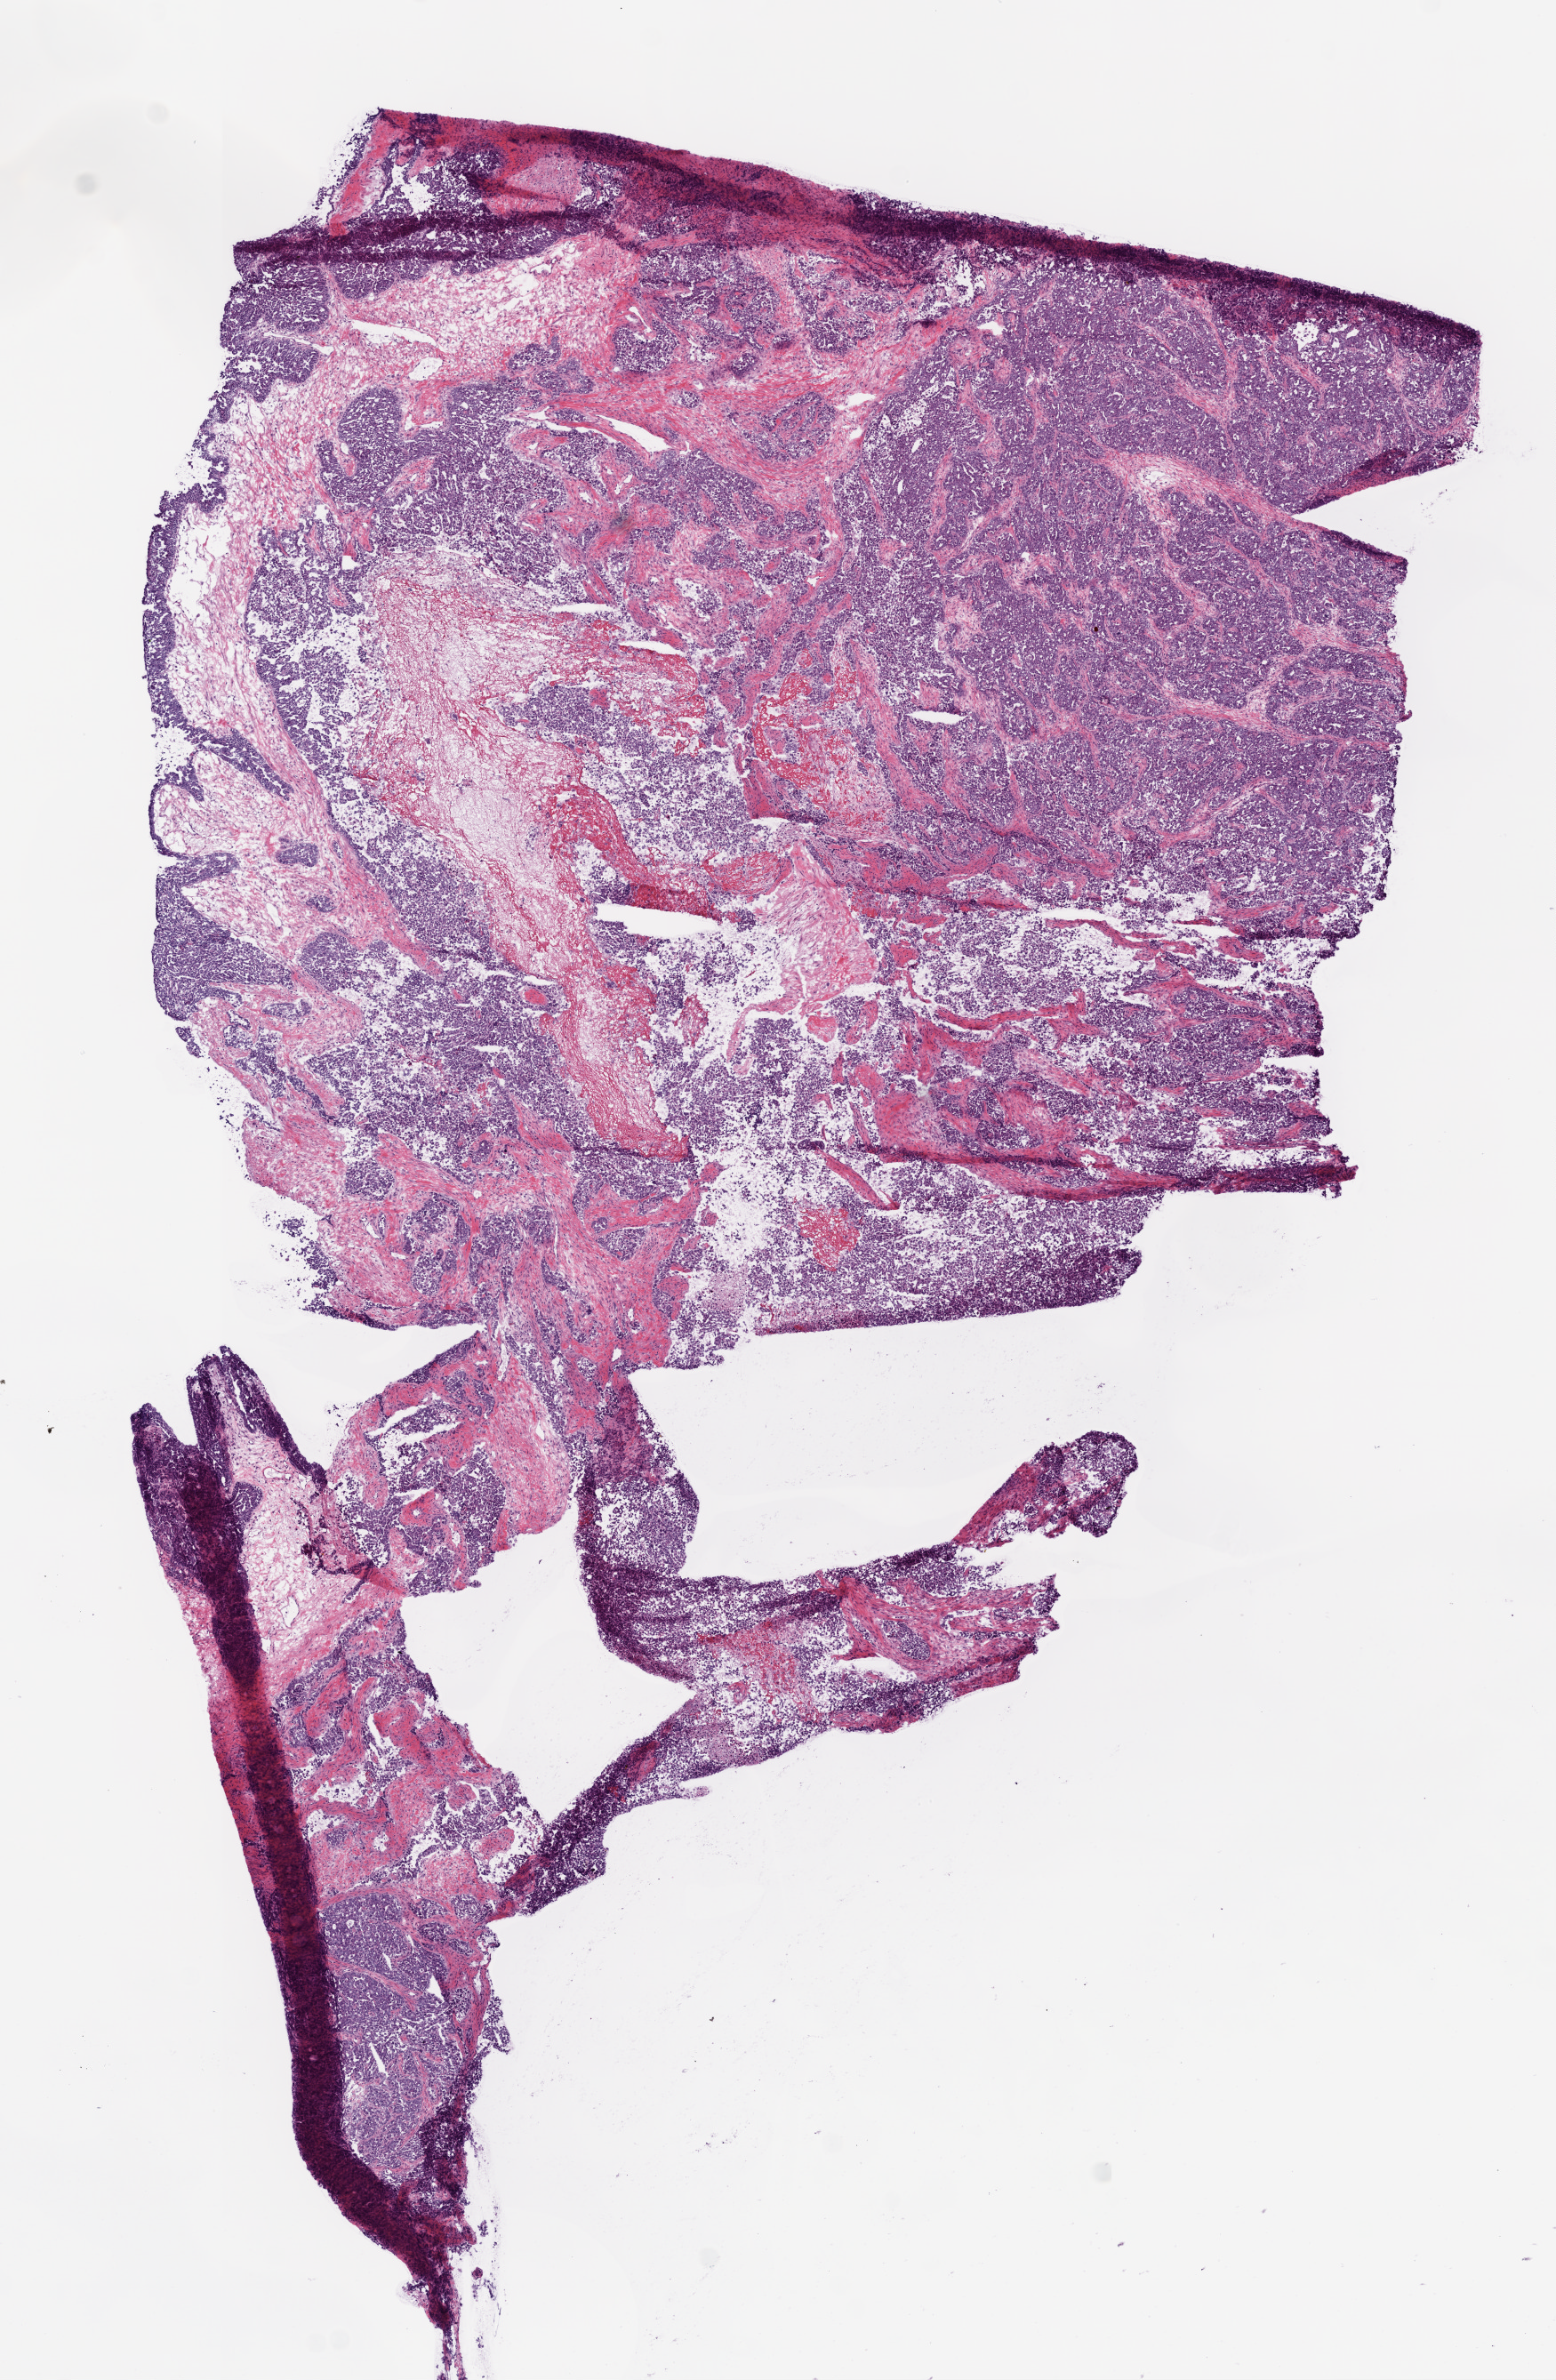
Digitized H&E tissue section (whole slide) — whole scanned area (about 7.0 x 10.7 mm) shown as a low-resolution overview; frozen section from the bottom of the tissue portion; primary tumour sample from the ovary. Female patient; age at initial diagnosis 67 years. Histologic grade: G3 (poorly differentiated). Slide review estimates, as recorded: tumour cells 35%, tumour nuclei 70%, normal cells 0%, stromal cells 60%, necrosis 5%.
FIGO stage: IIIC. Pathologic diagnosis: Serous cystadenocarcinoma, NOS. Laterality: bilateral.